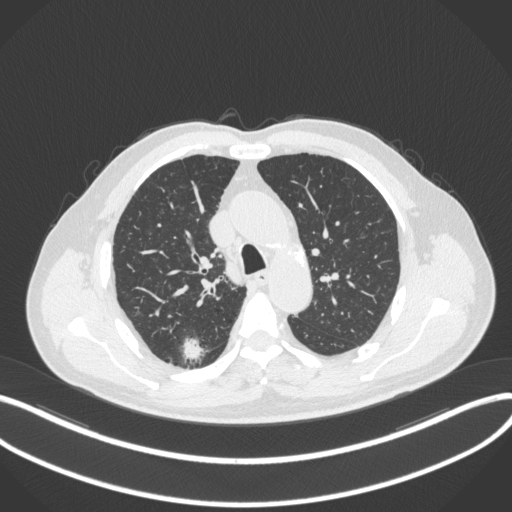
Chest CT, one axial slice; slice 264 of 366 in the series (ordered by position); lung window (W 1500 / L -600 HU); 1 mm slice thickness; 512 × 512 image matrix, field of view 400 × 400 mm. Male patient, age 69 years. From the clinical record (not read from this slice): clinical TNM (as recorded): T1b N0 M0; histopathological grade: G2-3.
Annotated regions visible in this slice (rectangle marked by the reading radiologist):
- lung tumour (recorded histology: adenocarcinoma): bounding box <182,333,206,368> (left, top, right, bottom; pixels)